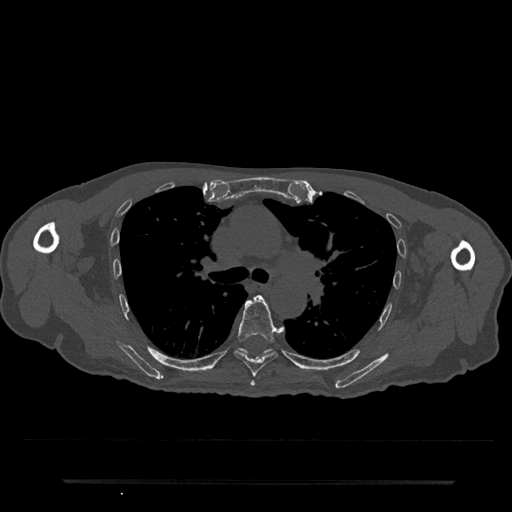
CT including the spine, one axial slice; position 524 of 797 along the scan axis; reconstruction kernel Br40s/3; 120 kVp; bone window (W 1800 / L 400 HU); 0.5 mm slice thickness; 512 × 512 image matrix. Male patient, age 74 years. Case-level facts recorded for this patient, not image findings: primary cancer: prostate.
Annotated regions visible in this slice (semi-automatic segmentation, software-assisted and operator-edited):
- T5 vertebra: bounding box [x1, y1, x2, y2] px = [250, 381, 255, 387]
- T6 vertebra: [234, 295, 283, 377]
- T7 vertebra: [239, 349, 271, 354]